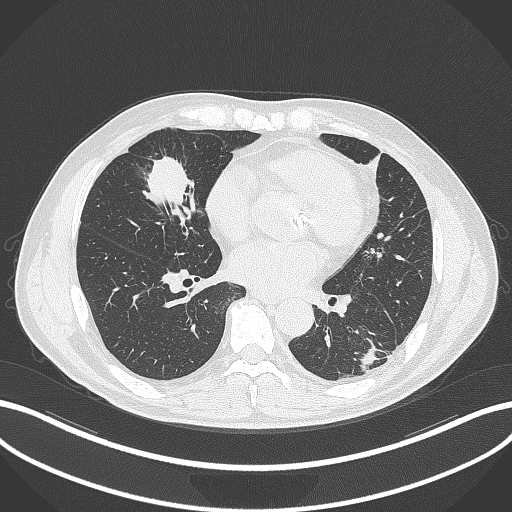
Chest CT, one axial slice; position 124 of 399 along the scan axis; reconstruction kernel B70f; 120 kVp; lung window (W 1500 / L -600 HU); 1 mm slice thickness; 512 × 512 image matrix. Male patient, age 59 years. Case-level facts recorded for this patient, not image findings: clinical TNM (as recorded): T2a N1 M0.
Outlined on this slice (bounding box drawn by a radiologist):
- lung tumour (recorded histology: adenocarcinoma): bounding box <140,152,199,227> (left, top, right, bottom; pixels)